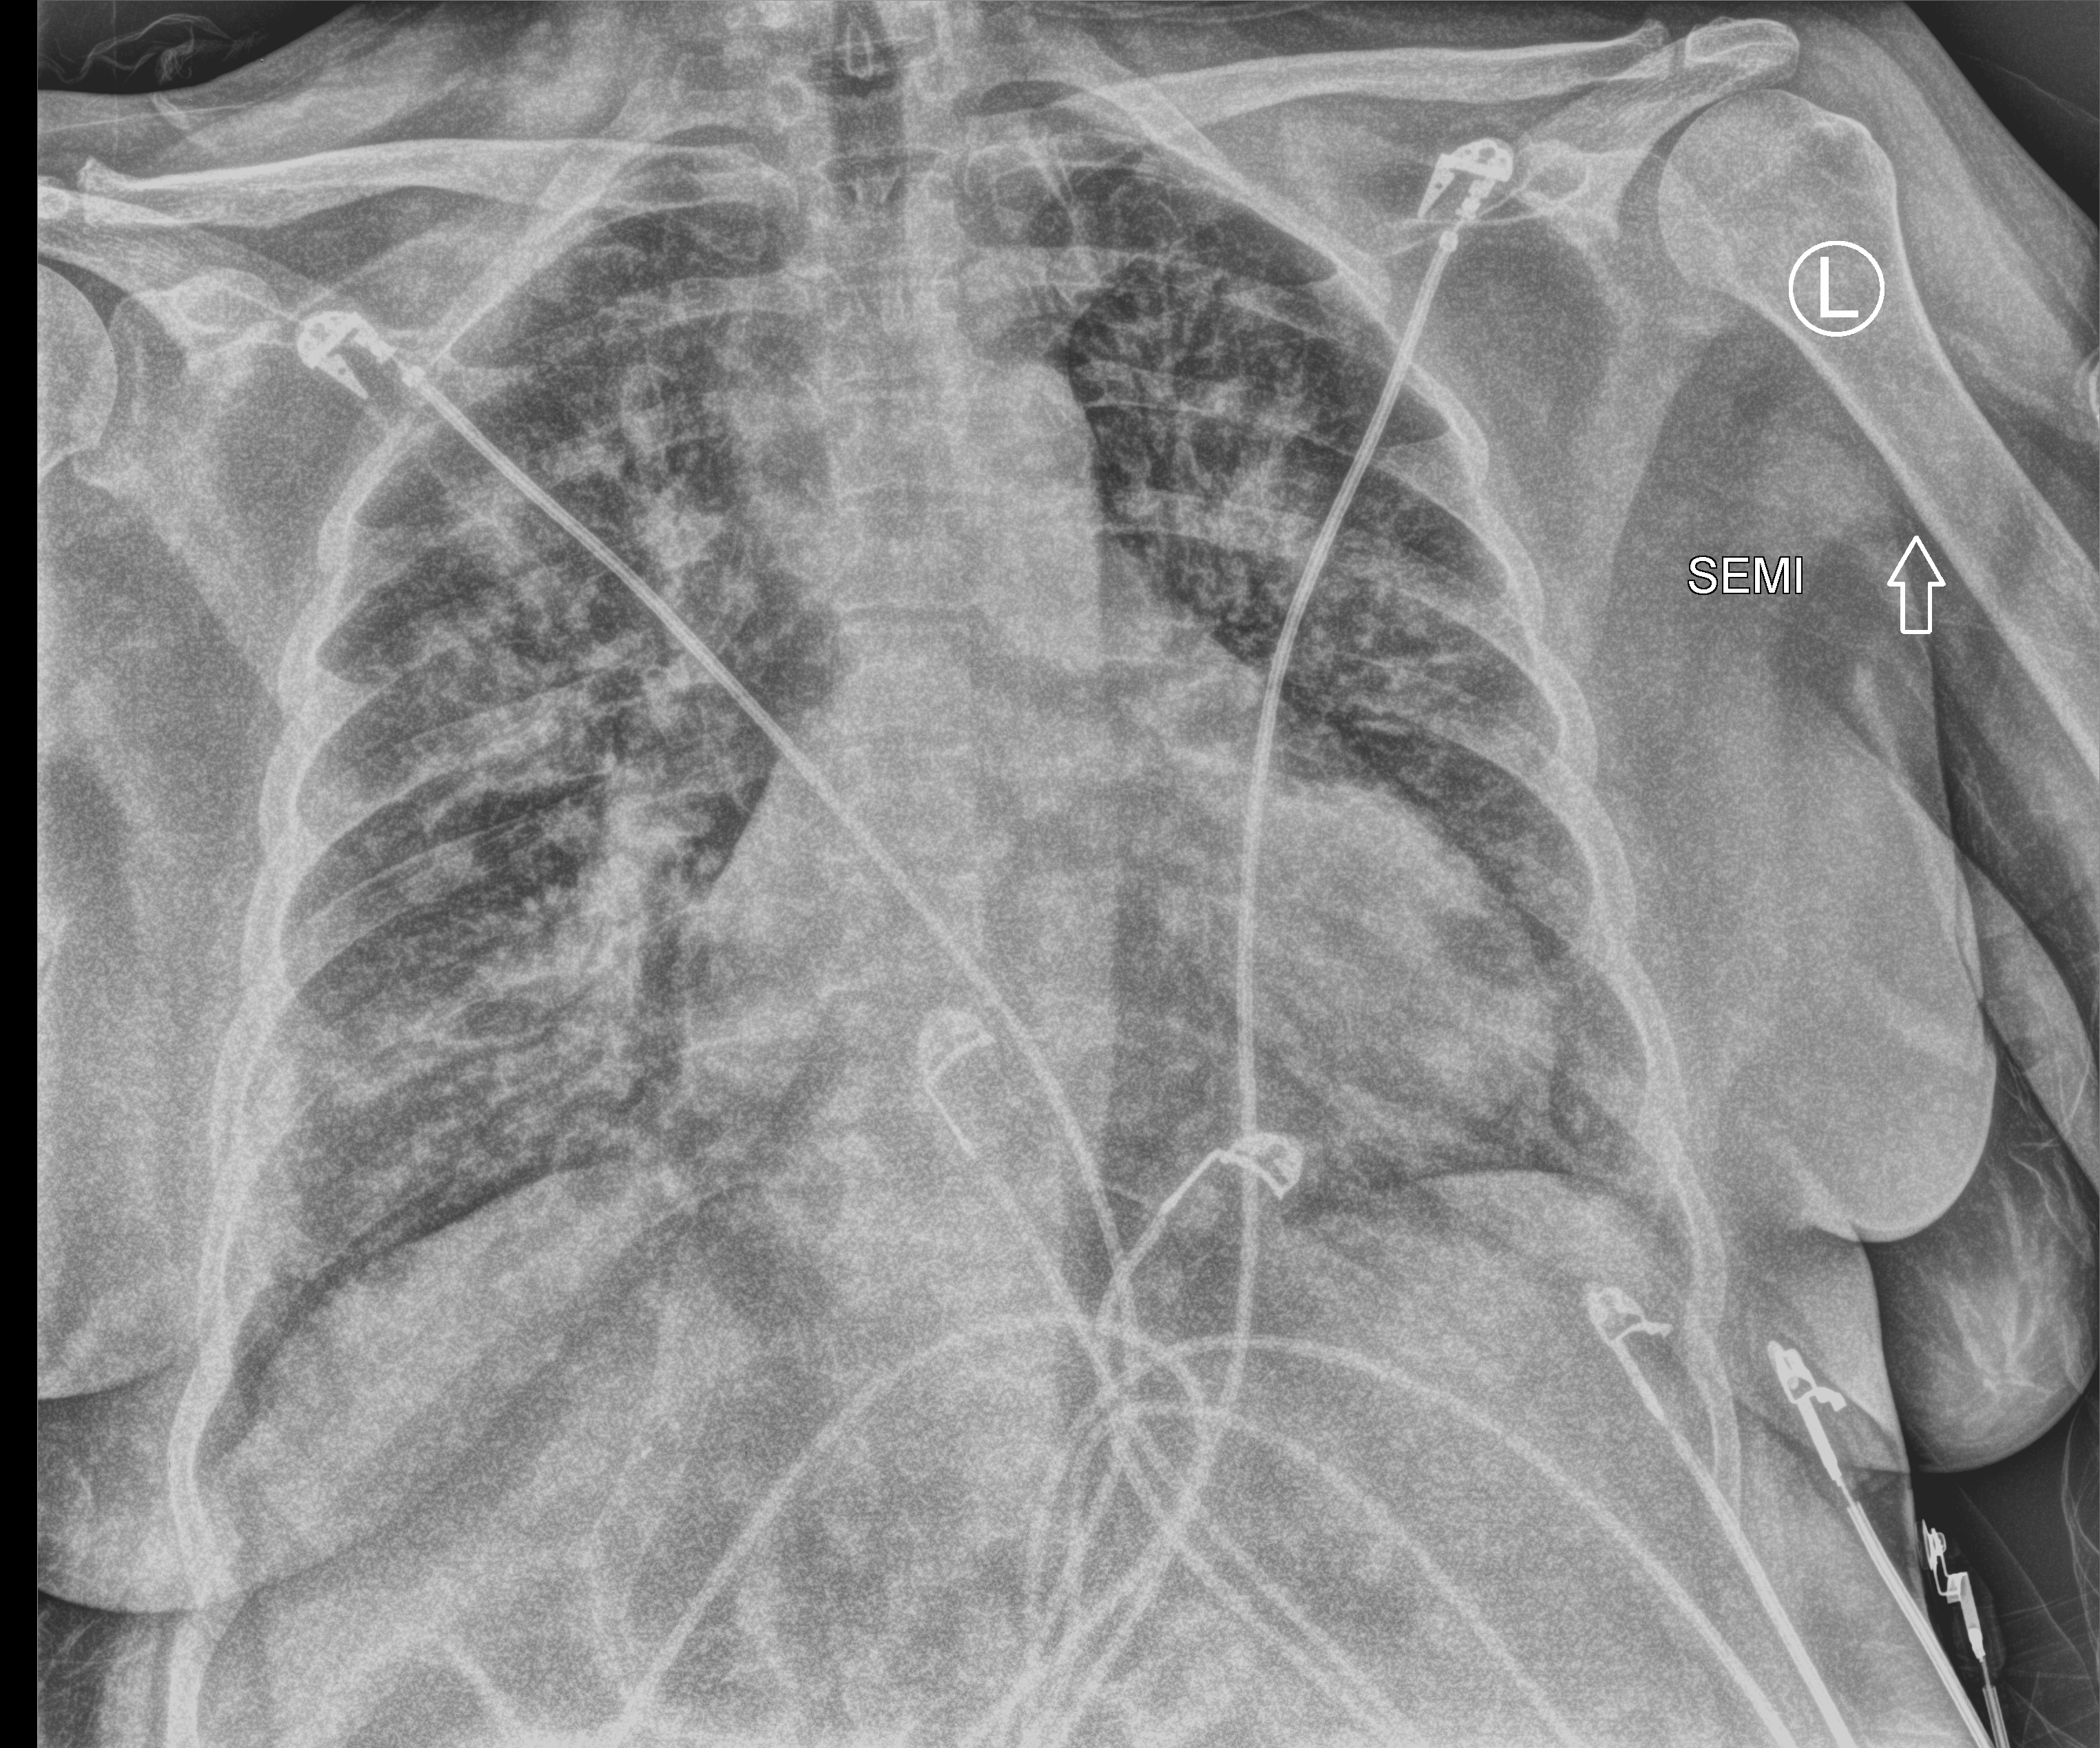
Chest X-ray (portable), anteroposterior (AP) projection. Female patient hospitalised with COVID-19, age 60–74 years.
Admission-level facts for this patient (not findings on this image; timing relative to this image not recorded):
- admitted to intensive care during this hospital stay: yes
- COPD (admission record): no
- mechanically ventilated during this hospital stay: no